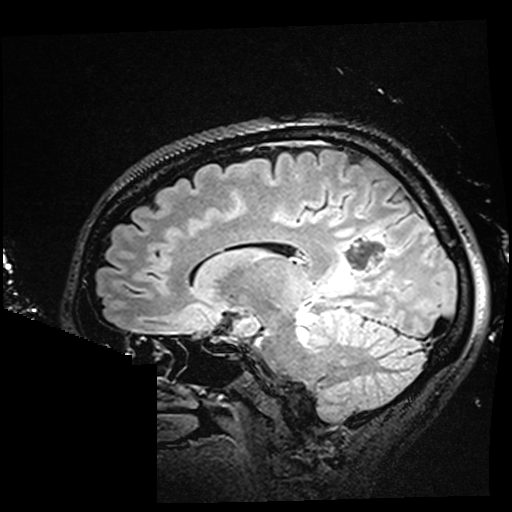
Brain MRI from a brain-tumour surgery series, one sagittal slice. Slice 104 of 176 in the series (ordered by position). T2 FLAIR. 1 mm slice thickness. 512 × 512 image matrix, field of view 250 × 250 mm. From the clinical record (not read from this slice): histopathology: Oligodendroglioma; WHO grade: 2; IDH mutation: yes.
Structures marked on this image (expert manual segmentation):
- residual tumour: box from (x=323, y=239) to (x=367, y=296) px